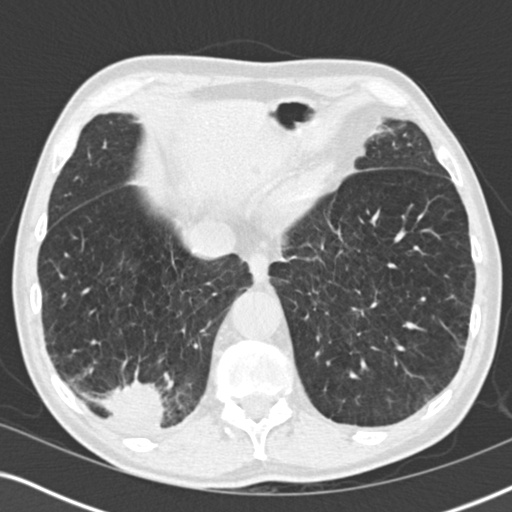
Low-dose screening chest CT, one axial slice. Slice 55 of 196 in the series (ordered by position). Reconstruction kernel B30f. 120 kVp. Lung window (W 1500 / L -600 HU). 2 mm slice thickness. 512 × 512 image matrix, field of view 330 × 330 mm.
Structures marked on this image (expert manual segmentation):
- lesion 3 (tumor, lower lobe of right lung): box from (x=101, y=381) to (x=166, y=430) px